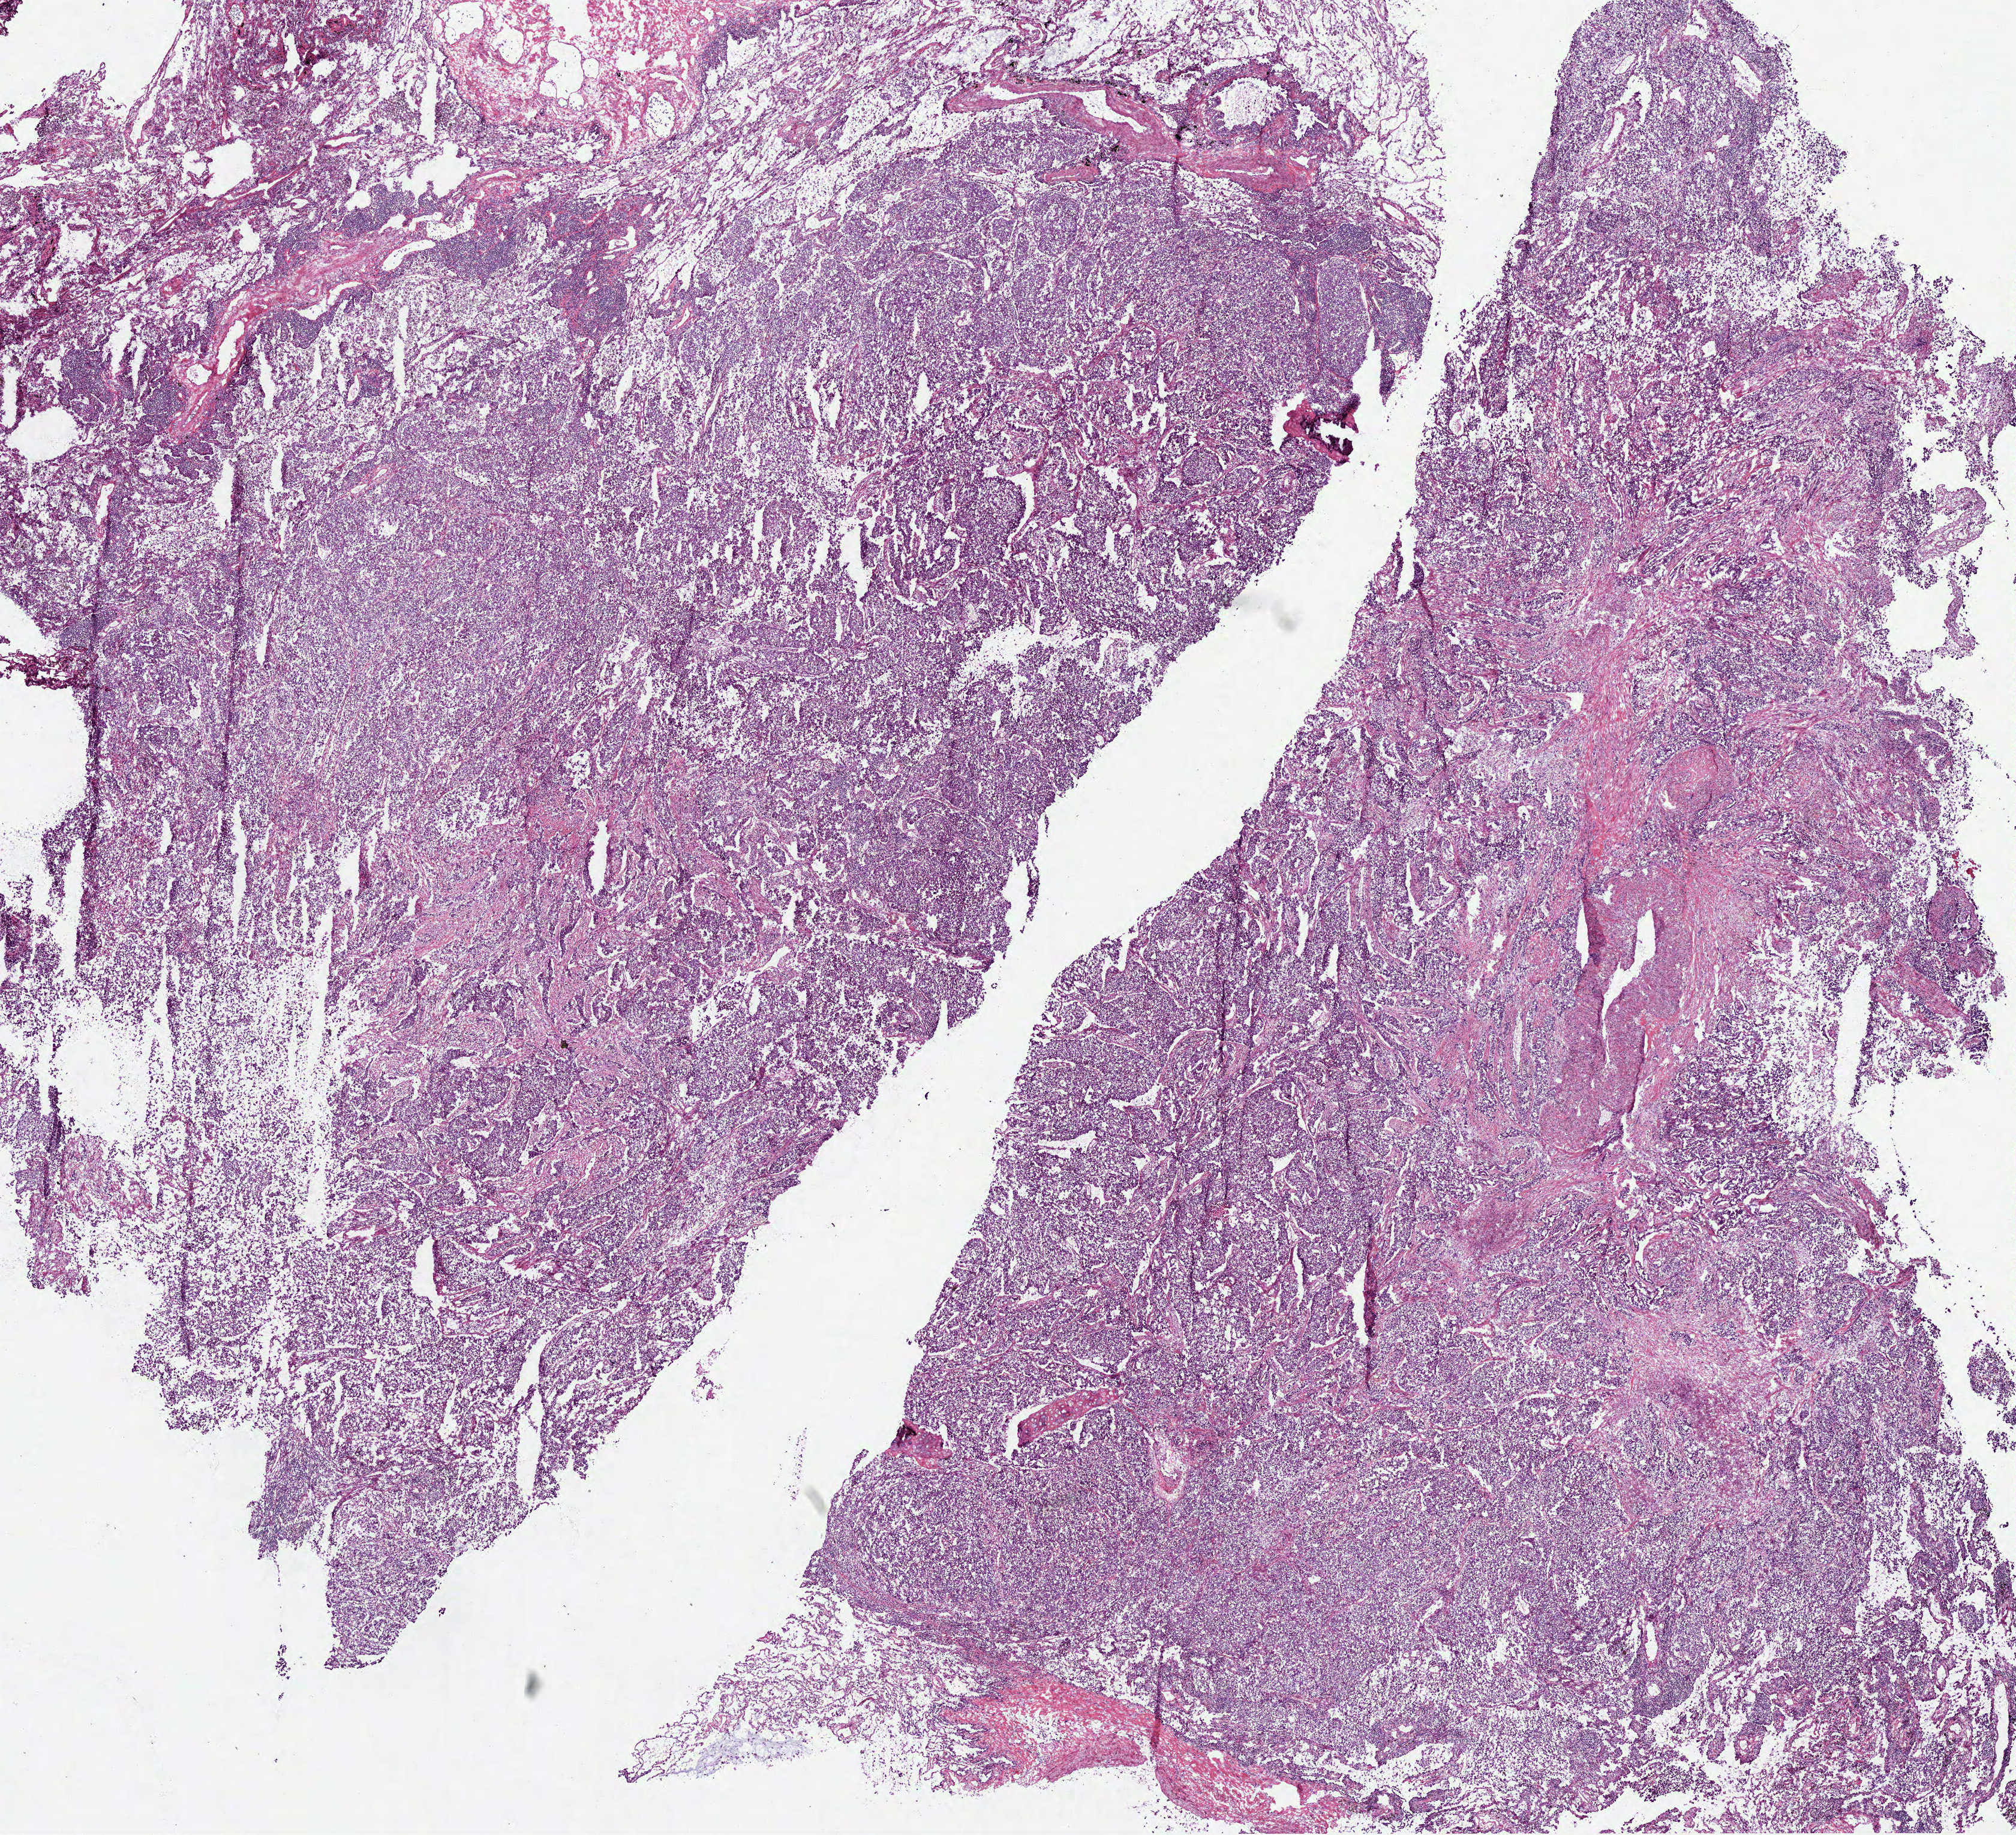
Whole-slide histology image, Hematoxylin and eosin (H&E) stained, low-resolution overview of the scanned area, about 13.6 x 12.3 mm; frozen section; lung, primary tumour sample. Patient: male, age at initial diagnosis 62 years. Composition of this section per pathologist review: tumour cells 80%, tumour nuclei 80%, normal cells 15%, stromal cells 0%, necrosis 5%. Infiltration values recorded for this section: lymphocyte infiltration 5%, monocyte infiltration 10%, neutrophil infiltration 1%.
• TNM: T1 N0 MX
• AJCC pathologic stage: IA
• laterality: right
• histologic diagnosis: Adenocarcinoma with mixed subtypes (upper lobe, lung)